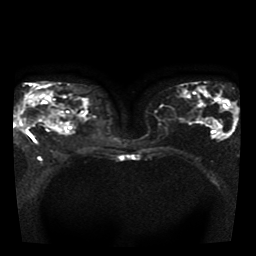
Breast MRI, one axial slice. Slice 19 of 41 in the series (ordered by position). Diffusion-weighted series; image 2 of 4 stored at this slice position (different b-values; order by instance number). 1.5 T. 256 × 256 image matrix, field of view 330 × 330 mm. Female patient.
Annotated regions visible in this slice (outlined manually by an expert reader):
- tumour on diffusion-weighted imaging: bounding box [x1, y1, x2, y2] px = [16, 101, 33, 132]